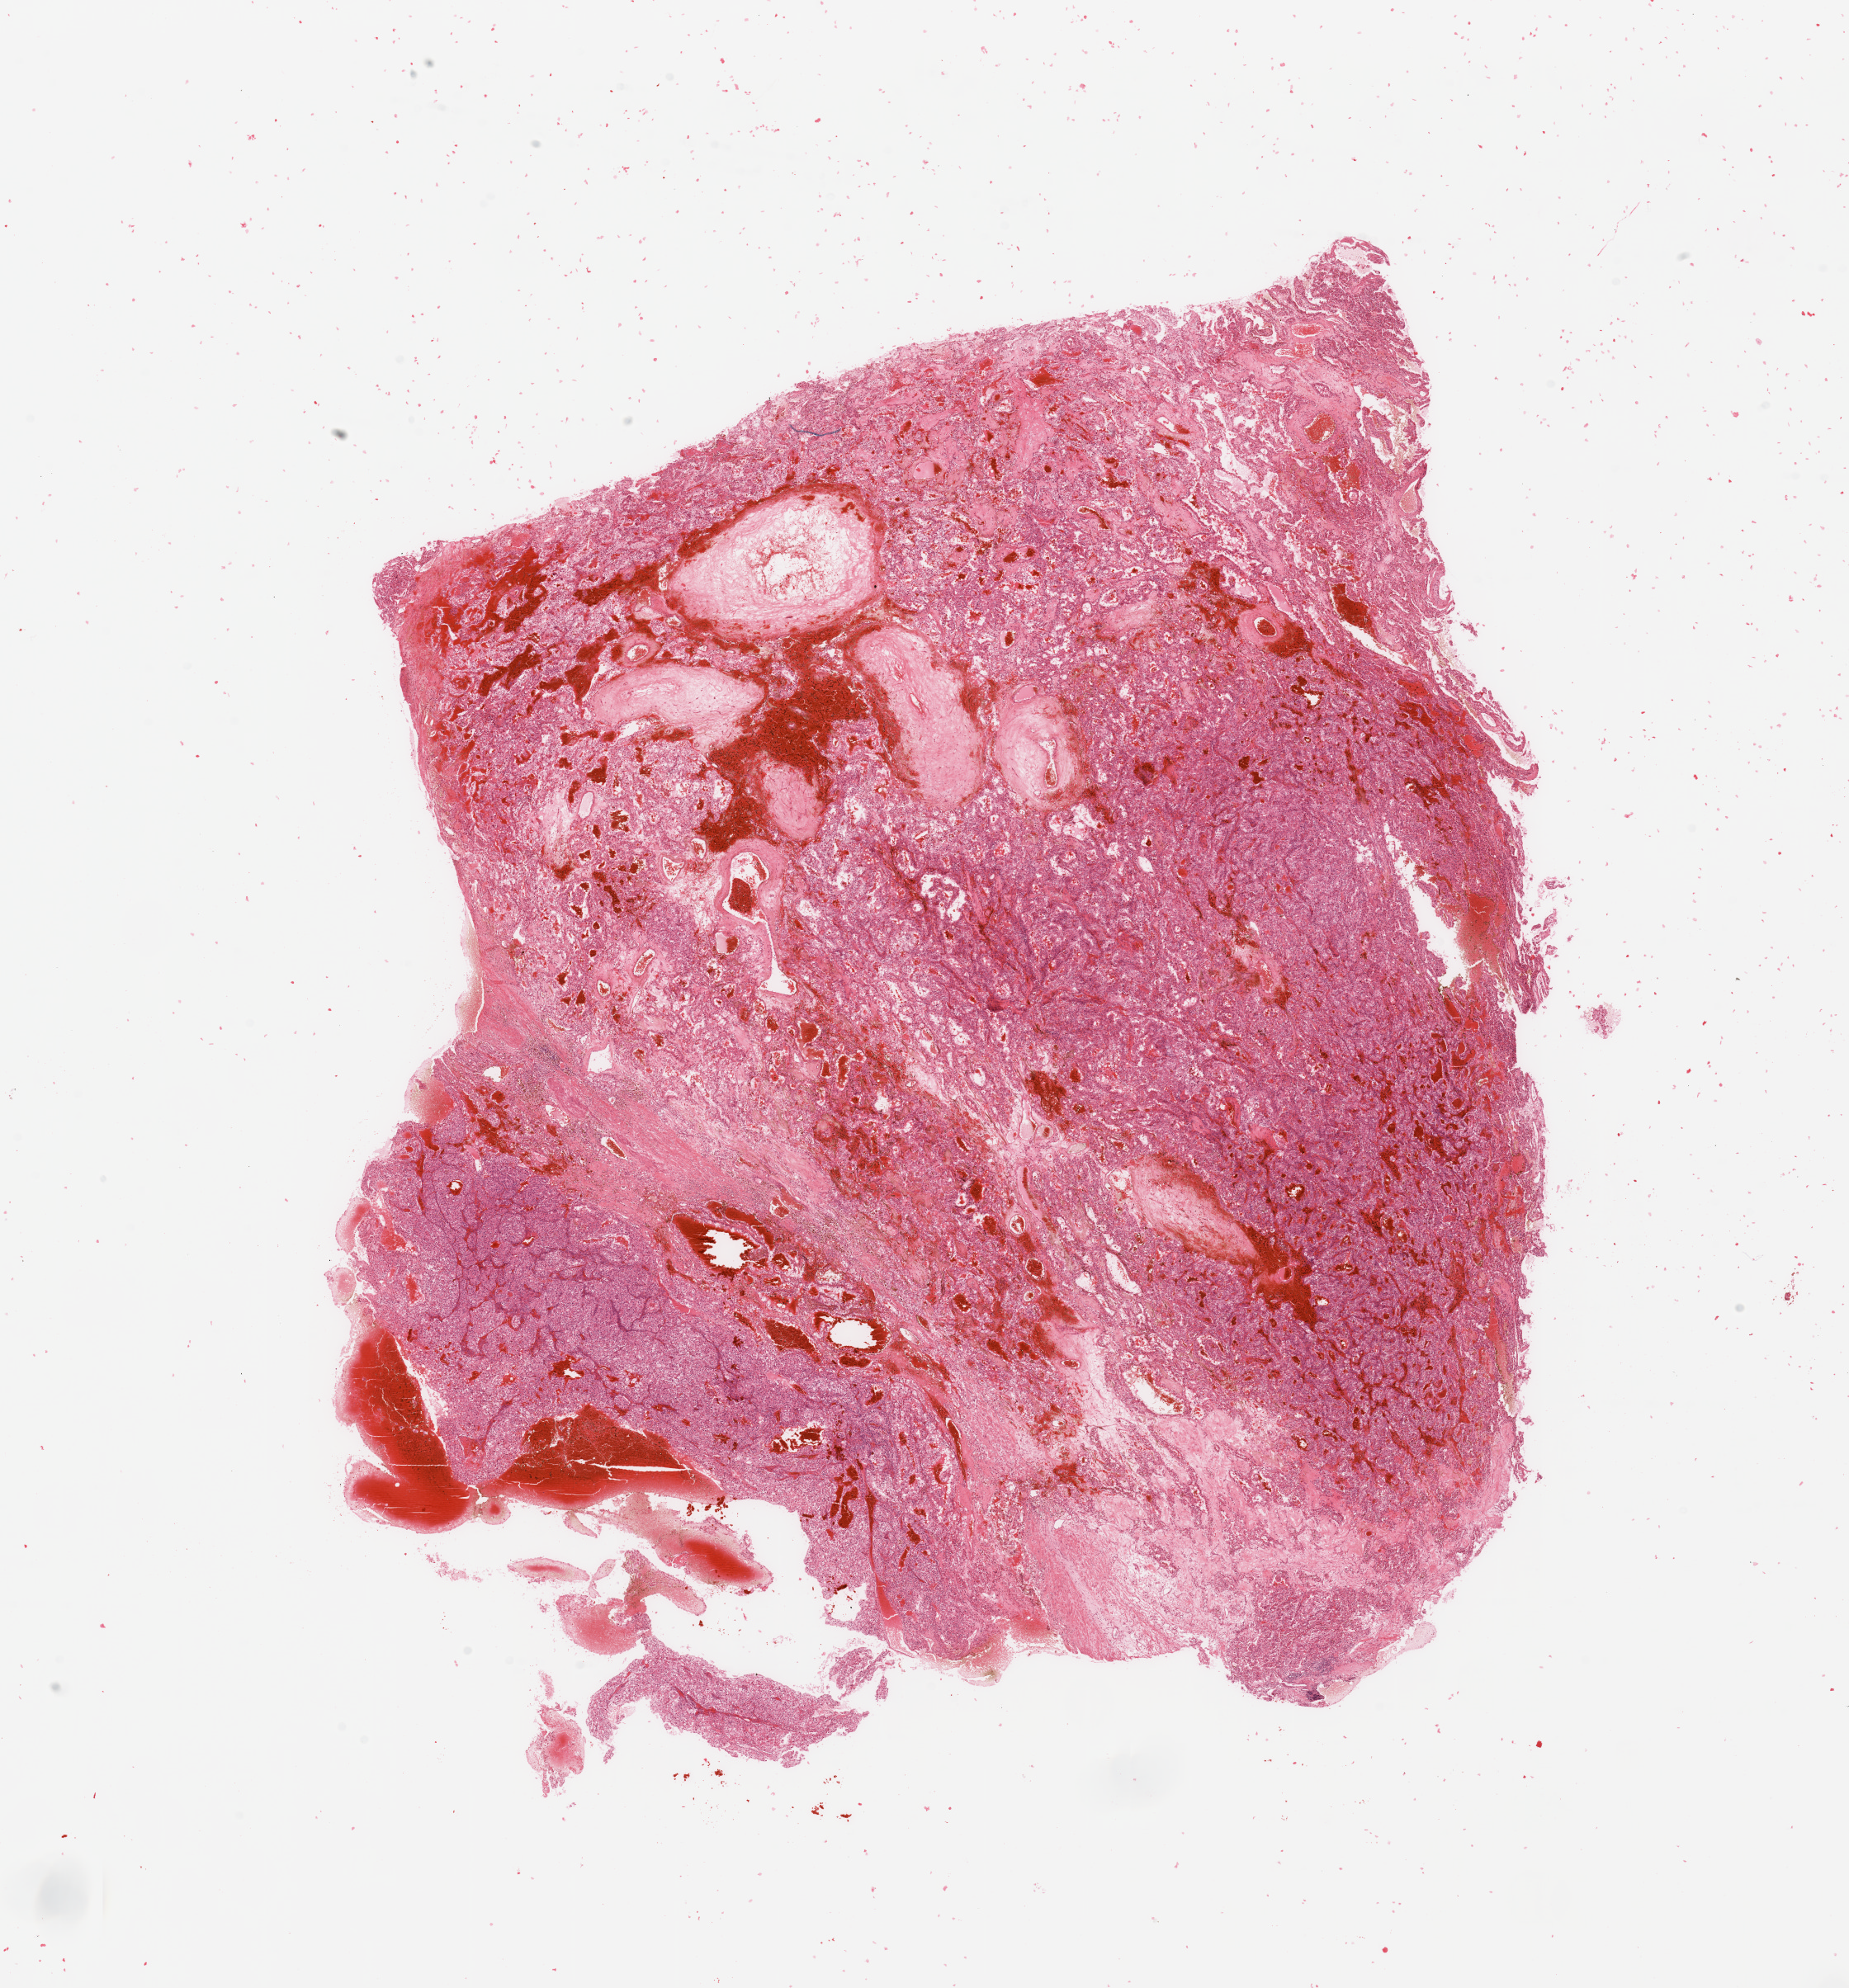
Whole-slide histology image, Hematoxylin and eosin (H&E) stained — low-resolution overview of the scanned area, about 17.7 x 19.1 mm (acquisition: 20x scan). Tumour tissue sample, sampled site: kidney. 52-year-old male patient.
Diagnosis: Renal cell carcinoma, NOS.